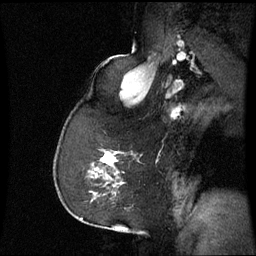
Breast MRI (dynamic contrast-enhanced), one sagittal slice. Position 42 of 60 along the scan axis. Dynamic contrast-enhanced series, image 2 of 3 at this slice position (ordered by acquisition). 1.5 T. TE 4.2 ms, TR 8.9 ms. 2.4 mm slice thickness. 256 × 256 image matrix. Female patient, age 59 years. Case-level facts recorded for this patient, not image findings: setting: breast cancer imaged before/during neoadjuvant chemotherapy; receptor status: triple-negative.
Annotated regions visible in this slice (semi-automatically segmented with operator editing):
- analysis volume of interest (the breast-tissue region the enhancement analysis was run in; not a lesion): bounding box <88,150,125,197> (left, top, right, bottom; pixels)
- tumour enhancement mask (voxels above the 70 % enhancement threshold inside the analysis volume of interest): <102,152,117,165>